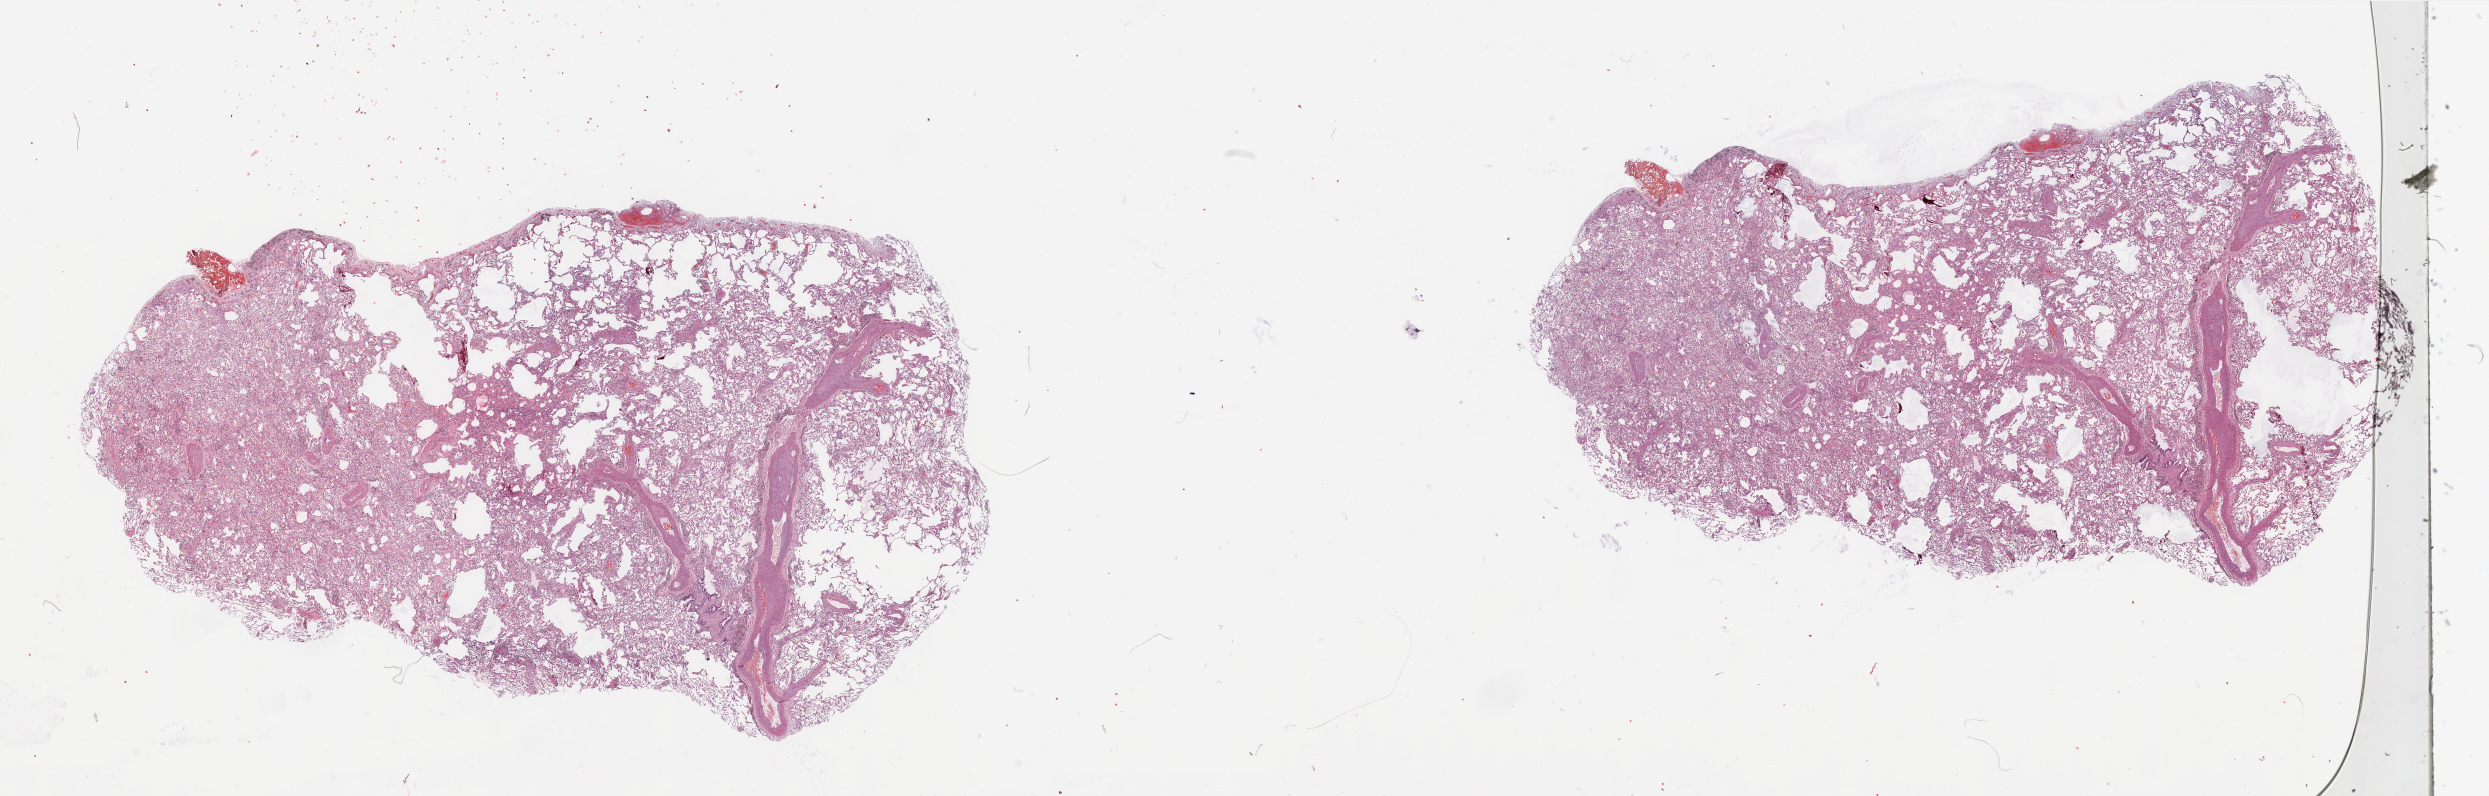
H&E whole-slide image — low-resolution overview of the scanned area, about 39.4 x 12.6 mm (from a 20x scan). Normal (non-tumour) tissue sample, sampled site: lung. 65-year-old male patient.
This section: normal (non-tumour) tissue from the same patient. Patient diagnosis: Adenocarcinoma, NOS.